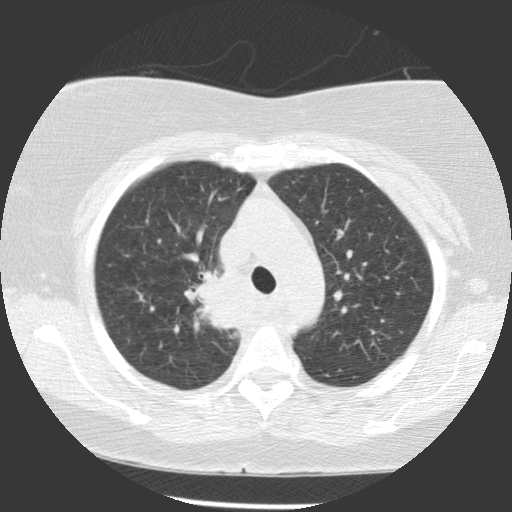
Chest CT (low-dose screening protocol), one axial image; baseline annual screen; lung window (W 1500 / L -600 HU); 2.5 mm slice thickness; standard (soft-tissue) reconstruction kernel (STANDARD); slice 85 of 116 in the series; 512 × 512 image matrix. Female participant, aged 63 years at enrolment.
Expert reader's lesion annotation, bounding box <193,264,253,325> (left, top, right, bottom; pixels). Reader record for this screening exam (exam-level; its link to the box is not recorded): non-calcified nodule or mass ≥4 mm, right upper lobe, 39 × 36 mm, spiculated (stellate) margins, soft tissue attenuation. Official screen result: positive, change unspecified: nodule(s) >= 4 mm or enlarging nodule(s), mass(es), or other non-specific abnormalities suspicious for lung cancer. Lung cancer was diagnosed 72 days after this screen: non-small cell carcinoma, right upper lobe, carina, right main stem bronchus, poorly differentiated (G3), stage IIIA (AJCC 6th edition), 66 mm at pathology.